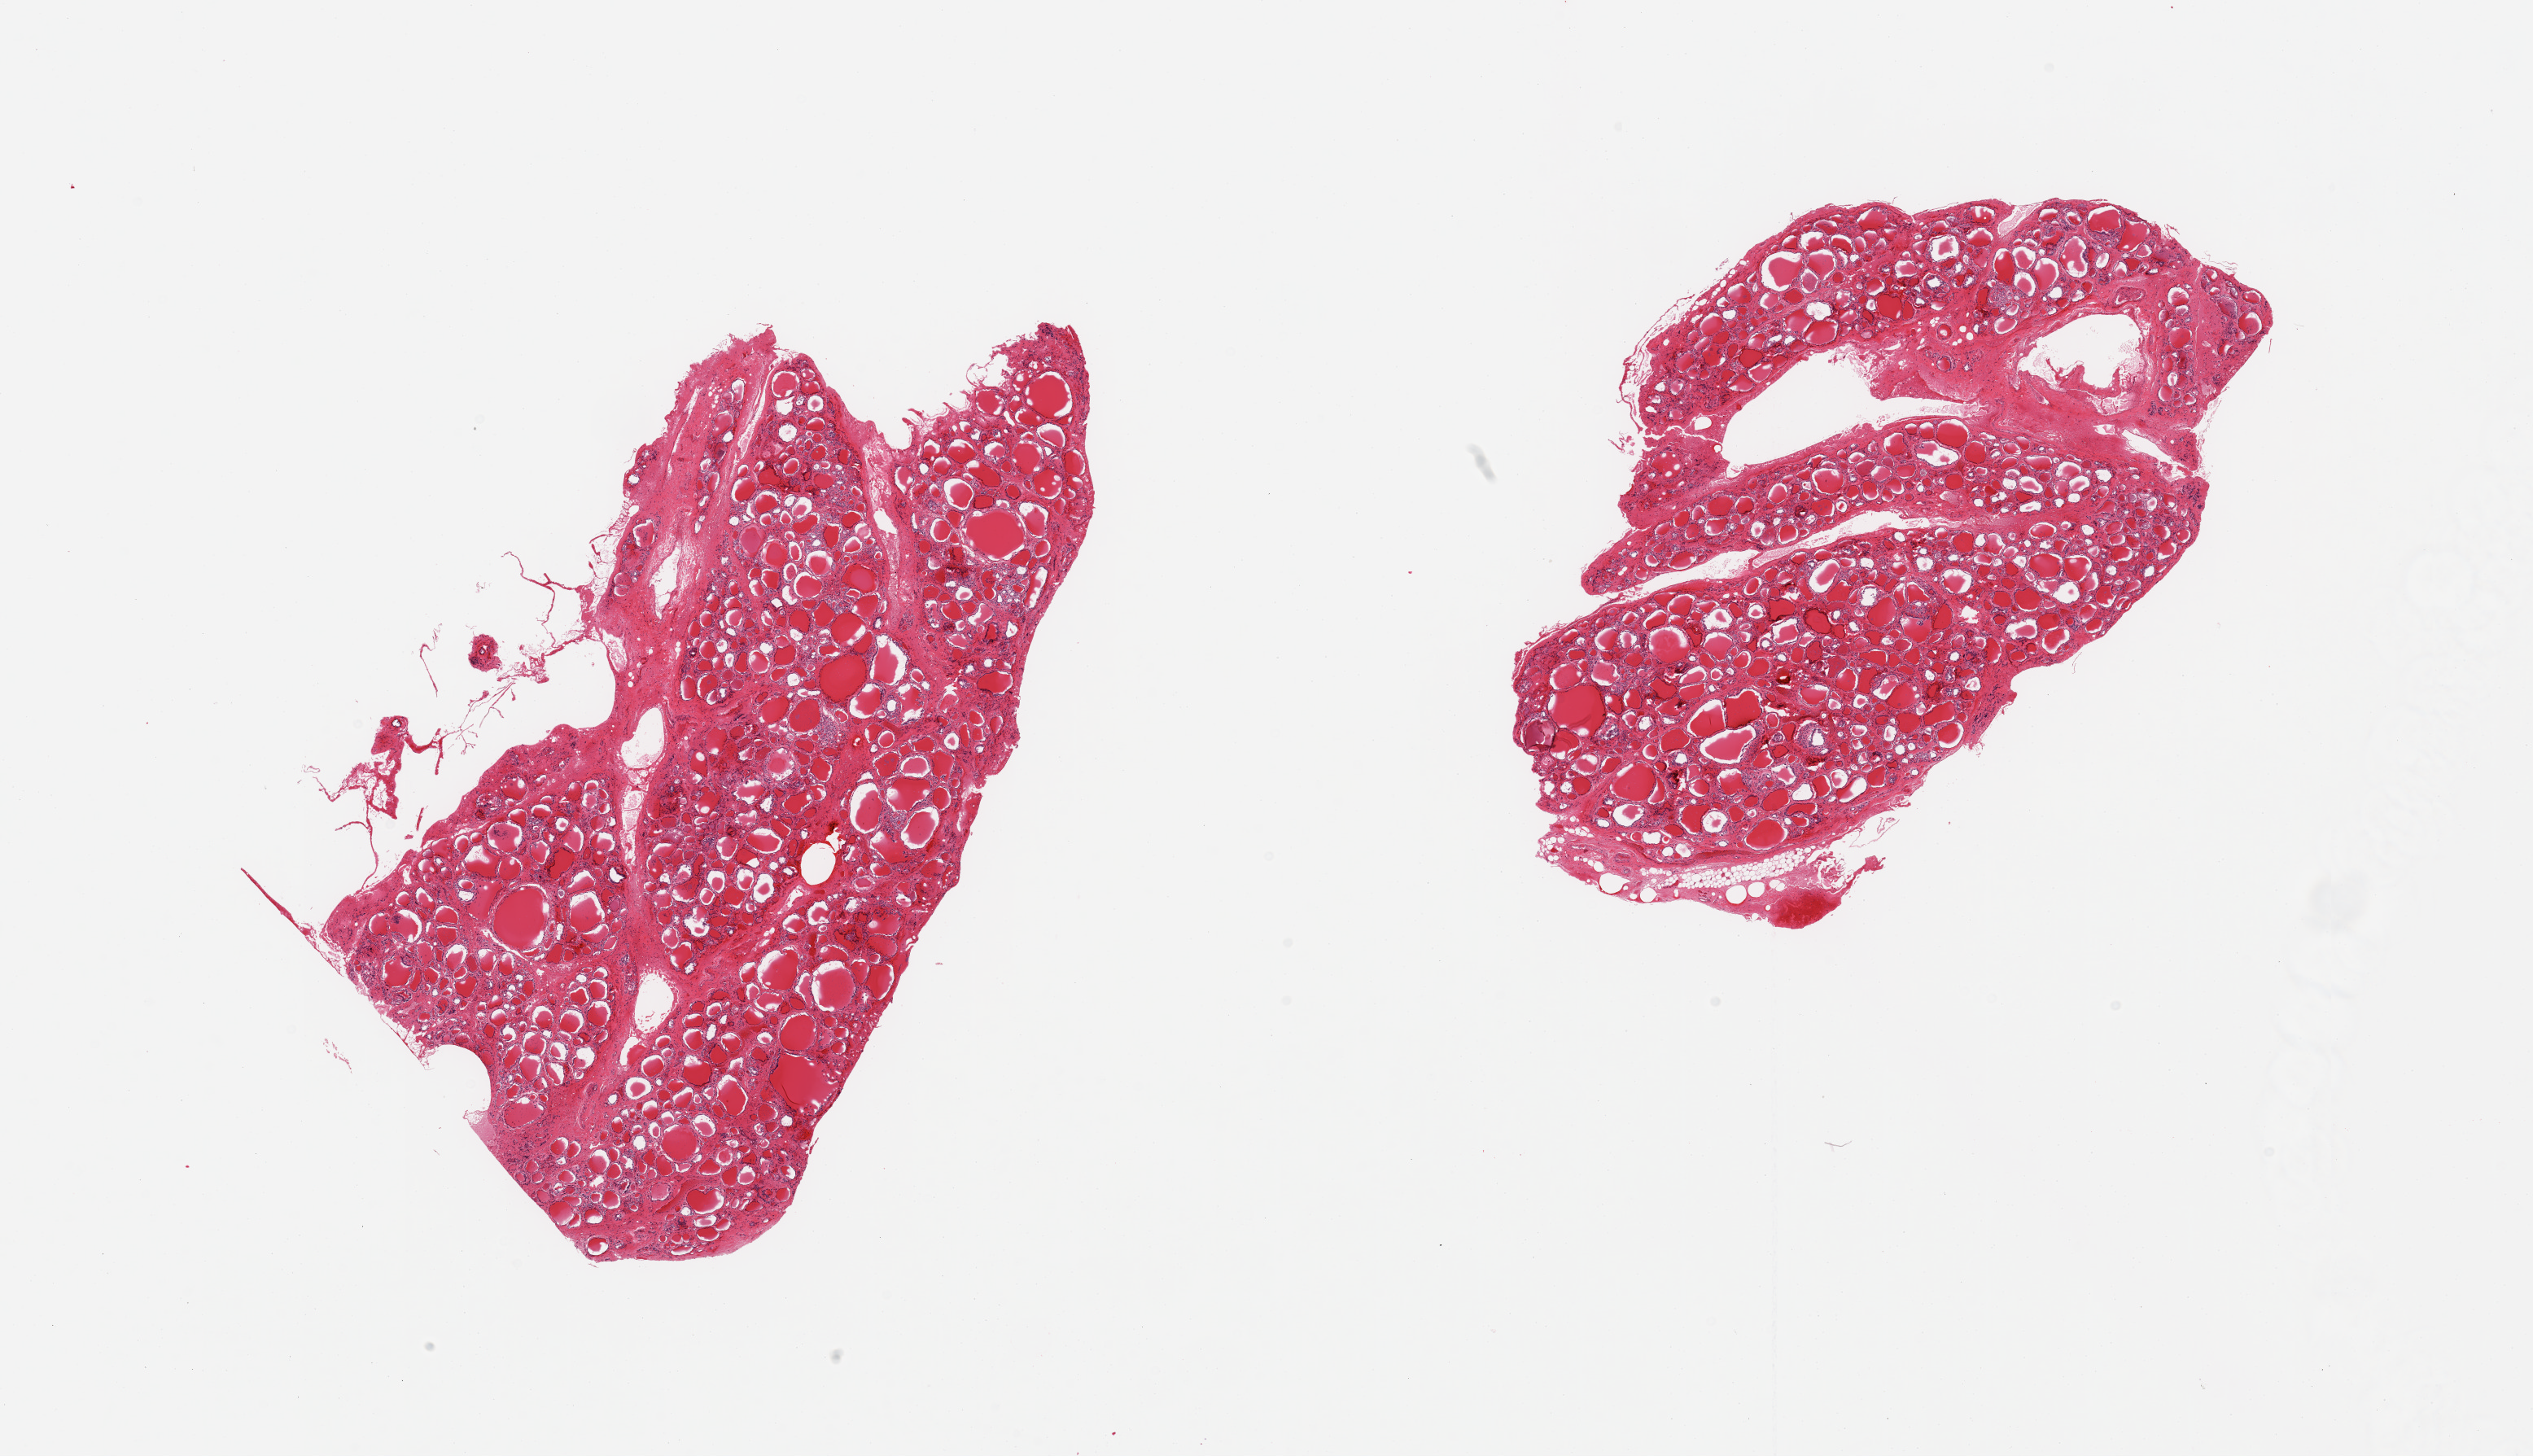
Hematoxylin and eosin (H&E) whole-slide image — low-resolution overview of the scanned area, about 24.6 x 14.1 mm (from a 20x scan), PAXgene-fixed, paraffin-embedded tissue, section of thyroid (target tissue), tissue donor sample. Donor: male.
Reviewer comment on this tissue sample: 2 pieces.